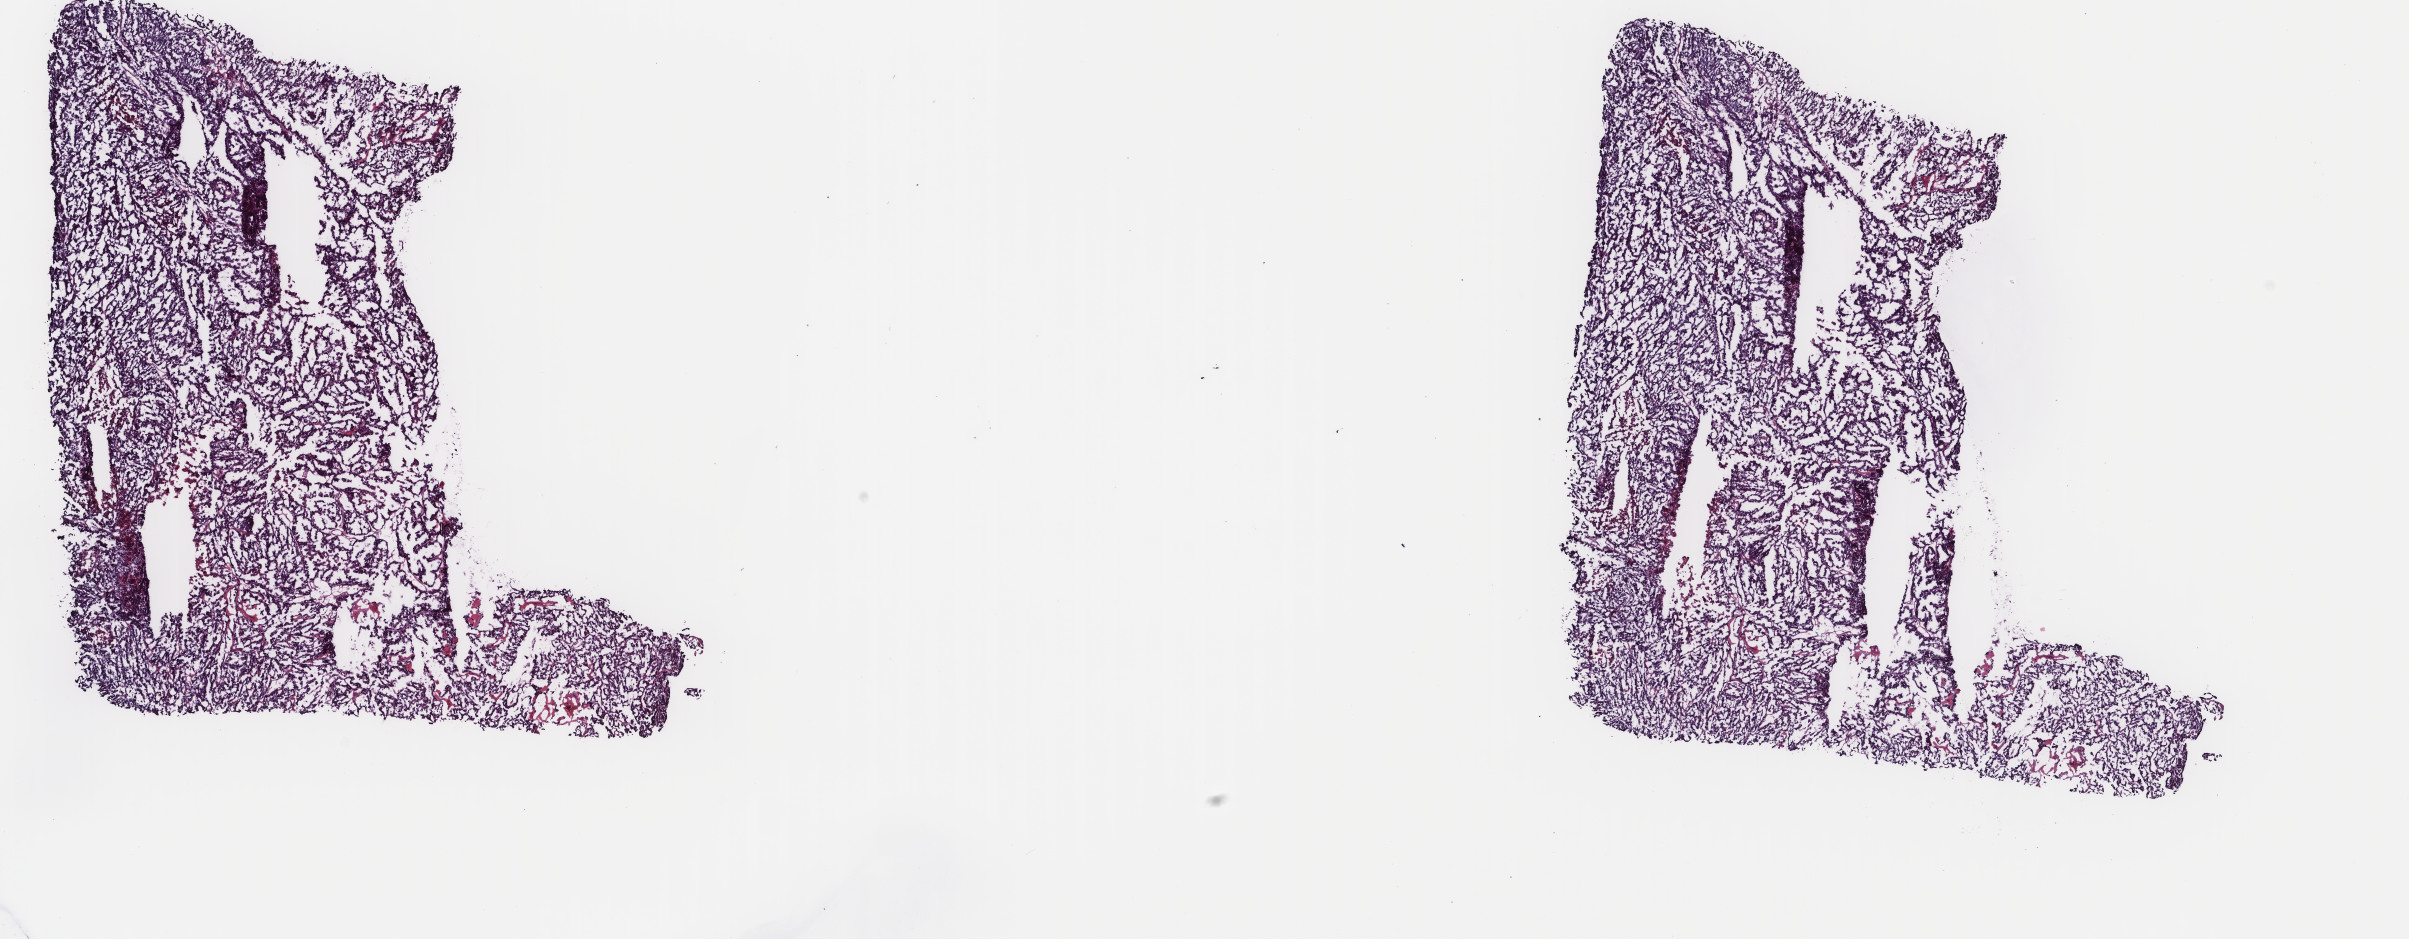
H&E whole-slide image — a low-resolution overview of the entire scanned area, about 19.1 x 7.5 mm (from a 40x scan), frozen section, uterus, primary tumour sample. Patient: female, age at initial diagnosis 68 years. Histologic grade: G3 (poorly differentiated). Pathologist review of this section (percent, as recorded): tumour cells 90%, tumour nuclei 90%, normal cells 0%, stromal cells 5%, necrosis 5%. Inflammatory infiltration, as recorded: lymphocyte infiltration 40%, monocyte infiltration 20%, neutrophil infiltration 20%.
Diagnosis: Serous cystadenocarcinoma, NOS (endometrium). FIGO stage: IA.